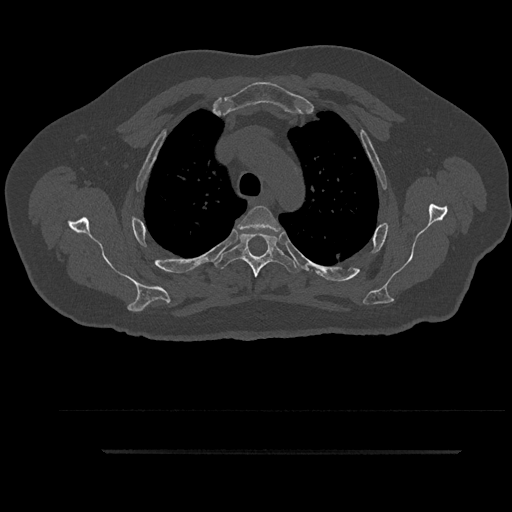
CT including the spine, one axial slice; slice 687 of 797 in the series (ordered by position); bone window (W 1800 / L 400 HU); 0.5 mm slice thickness; 512 × 512 image matrix, field of view 432 × 432 mm. Male patient, age 63 years. From the clinical record (not read from this slice): primary cancer: renal; vertebrae with lytic lesions (as recorded): T8.
Outlined on this slice (semi-automatically segmented with operator editing):
- T3 vertebra: bounding box (x1, y1, x2, y2) in pixels: (238, 206, 280, 236)
- T4 vertebra: (214, 233, 300, 278)